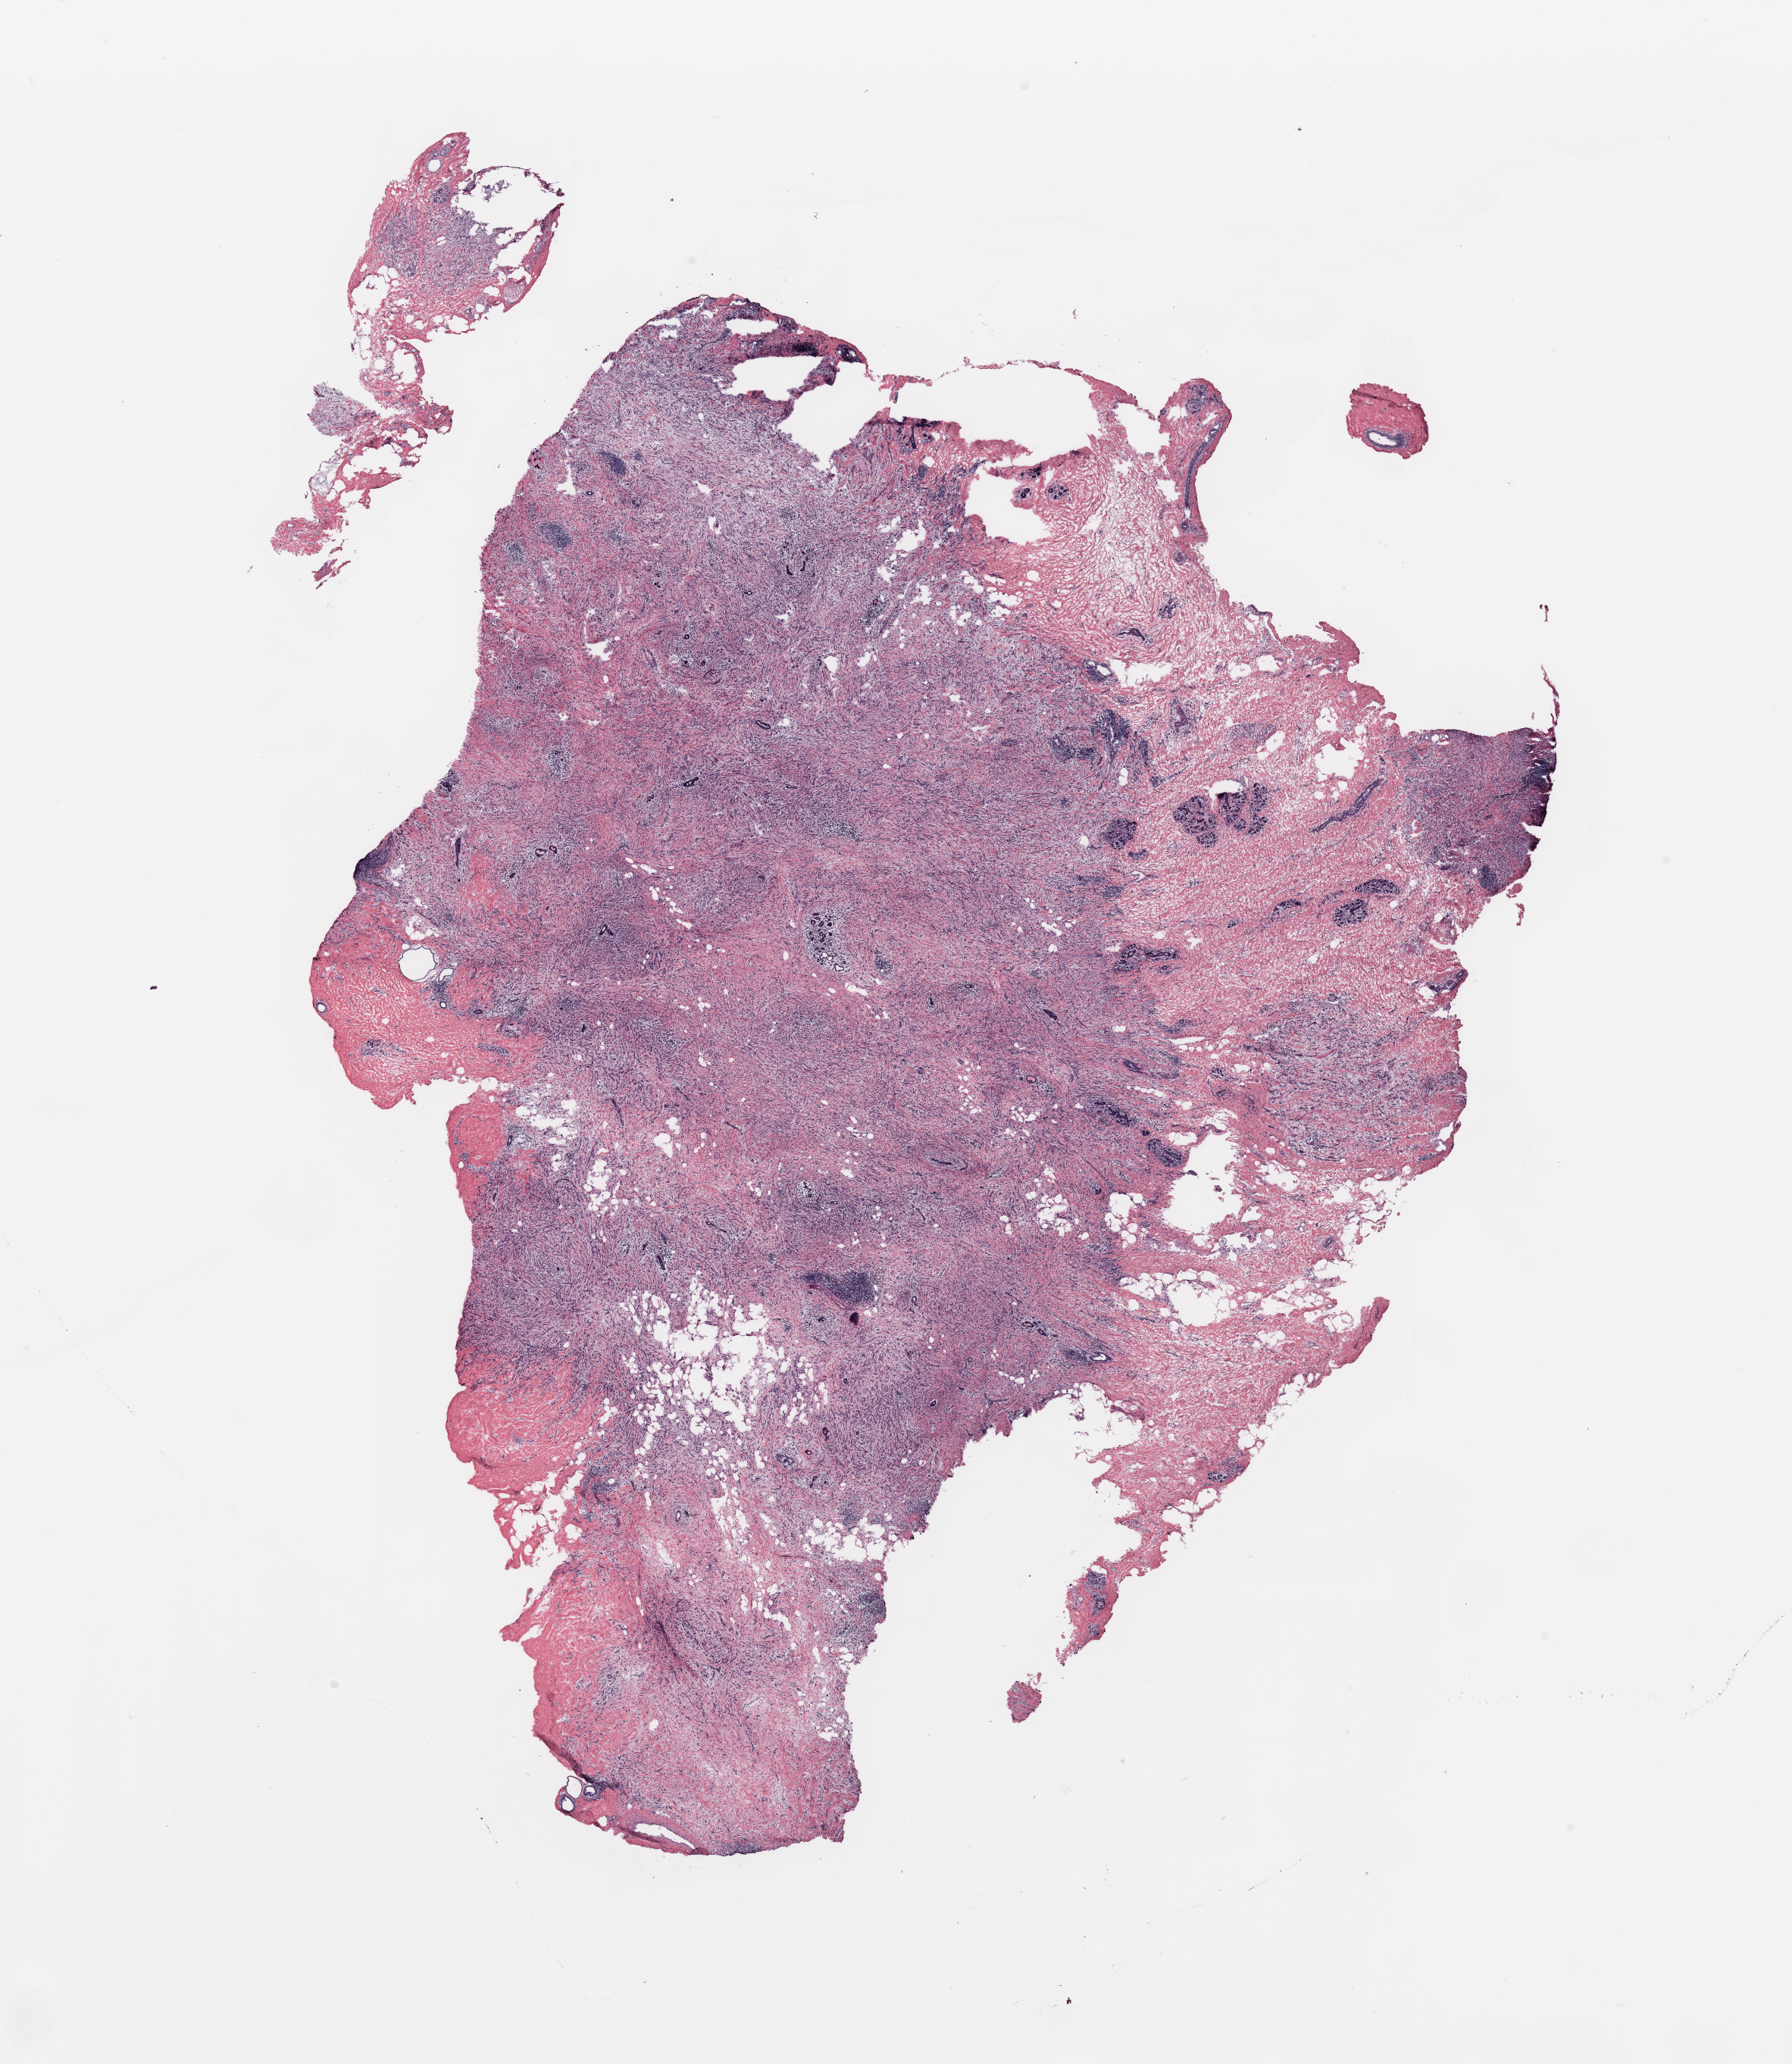
Digitized H&E tissue section (whole slide) — whole scanned area (about 18.7 x 21.5 mm, acquisition: 20x scan) shown as a low-resolution overview. Breast, tissue type not recorded.
Patient diagnosis (cohort enrolment): breast cancer (breast).